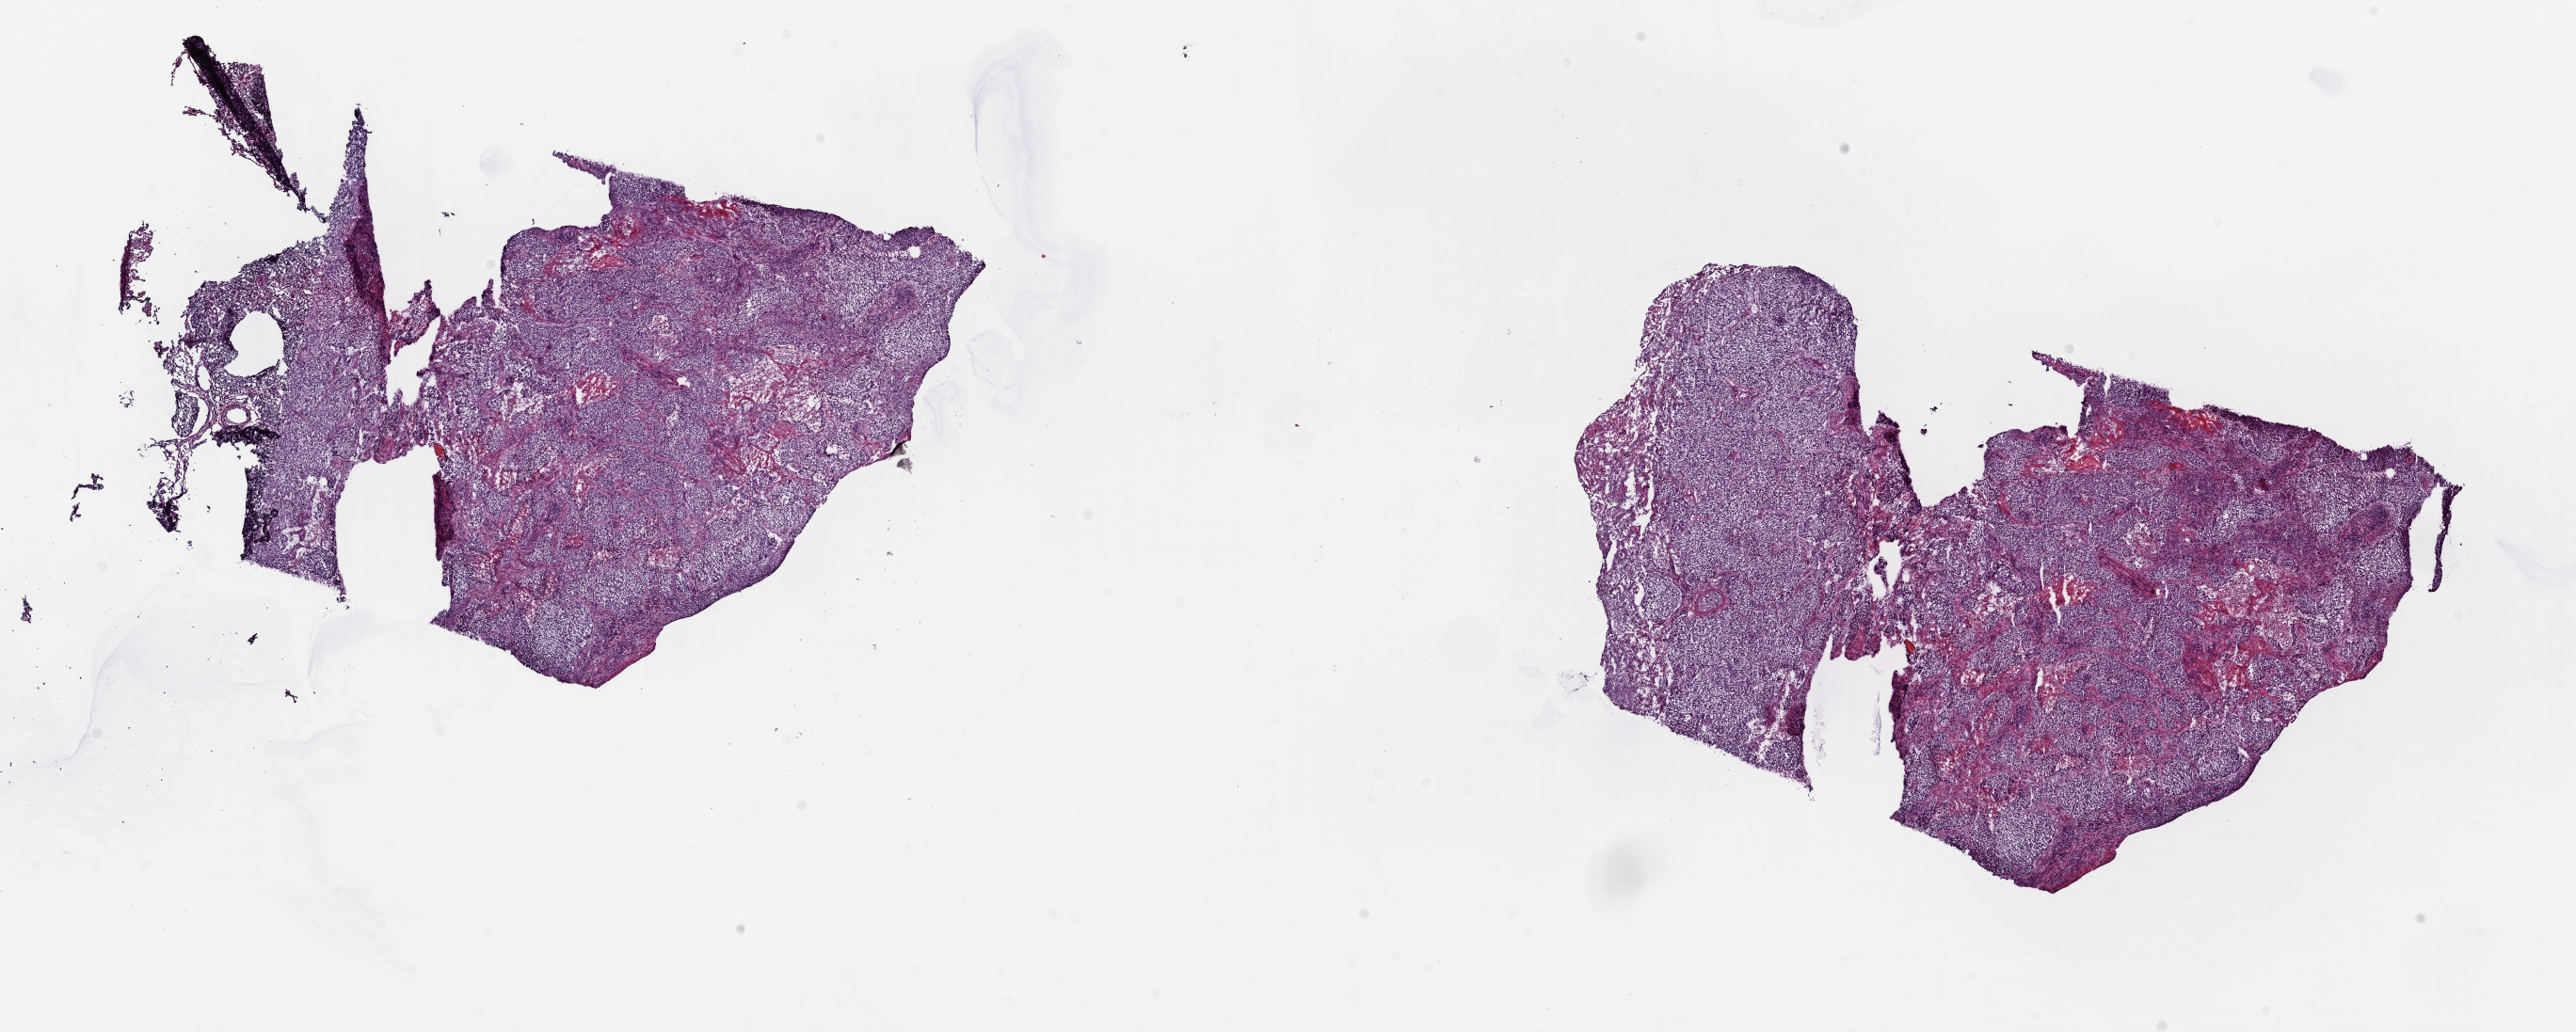
Digitized H&E-stained tissue section (whole slide) — a low-resolution overview of the entire scanned area, about 21.6 x 8.7 mm, frozen section from the top of the tissue portion, sample: primary tumour, lung. Patient sex: female.
Diagnosis: Squamous cell carcinoma, NOS (lower lobe, lung).